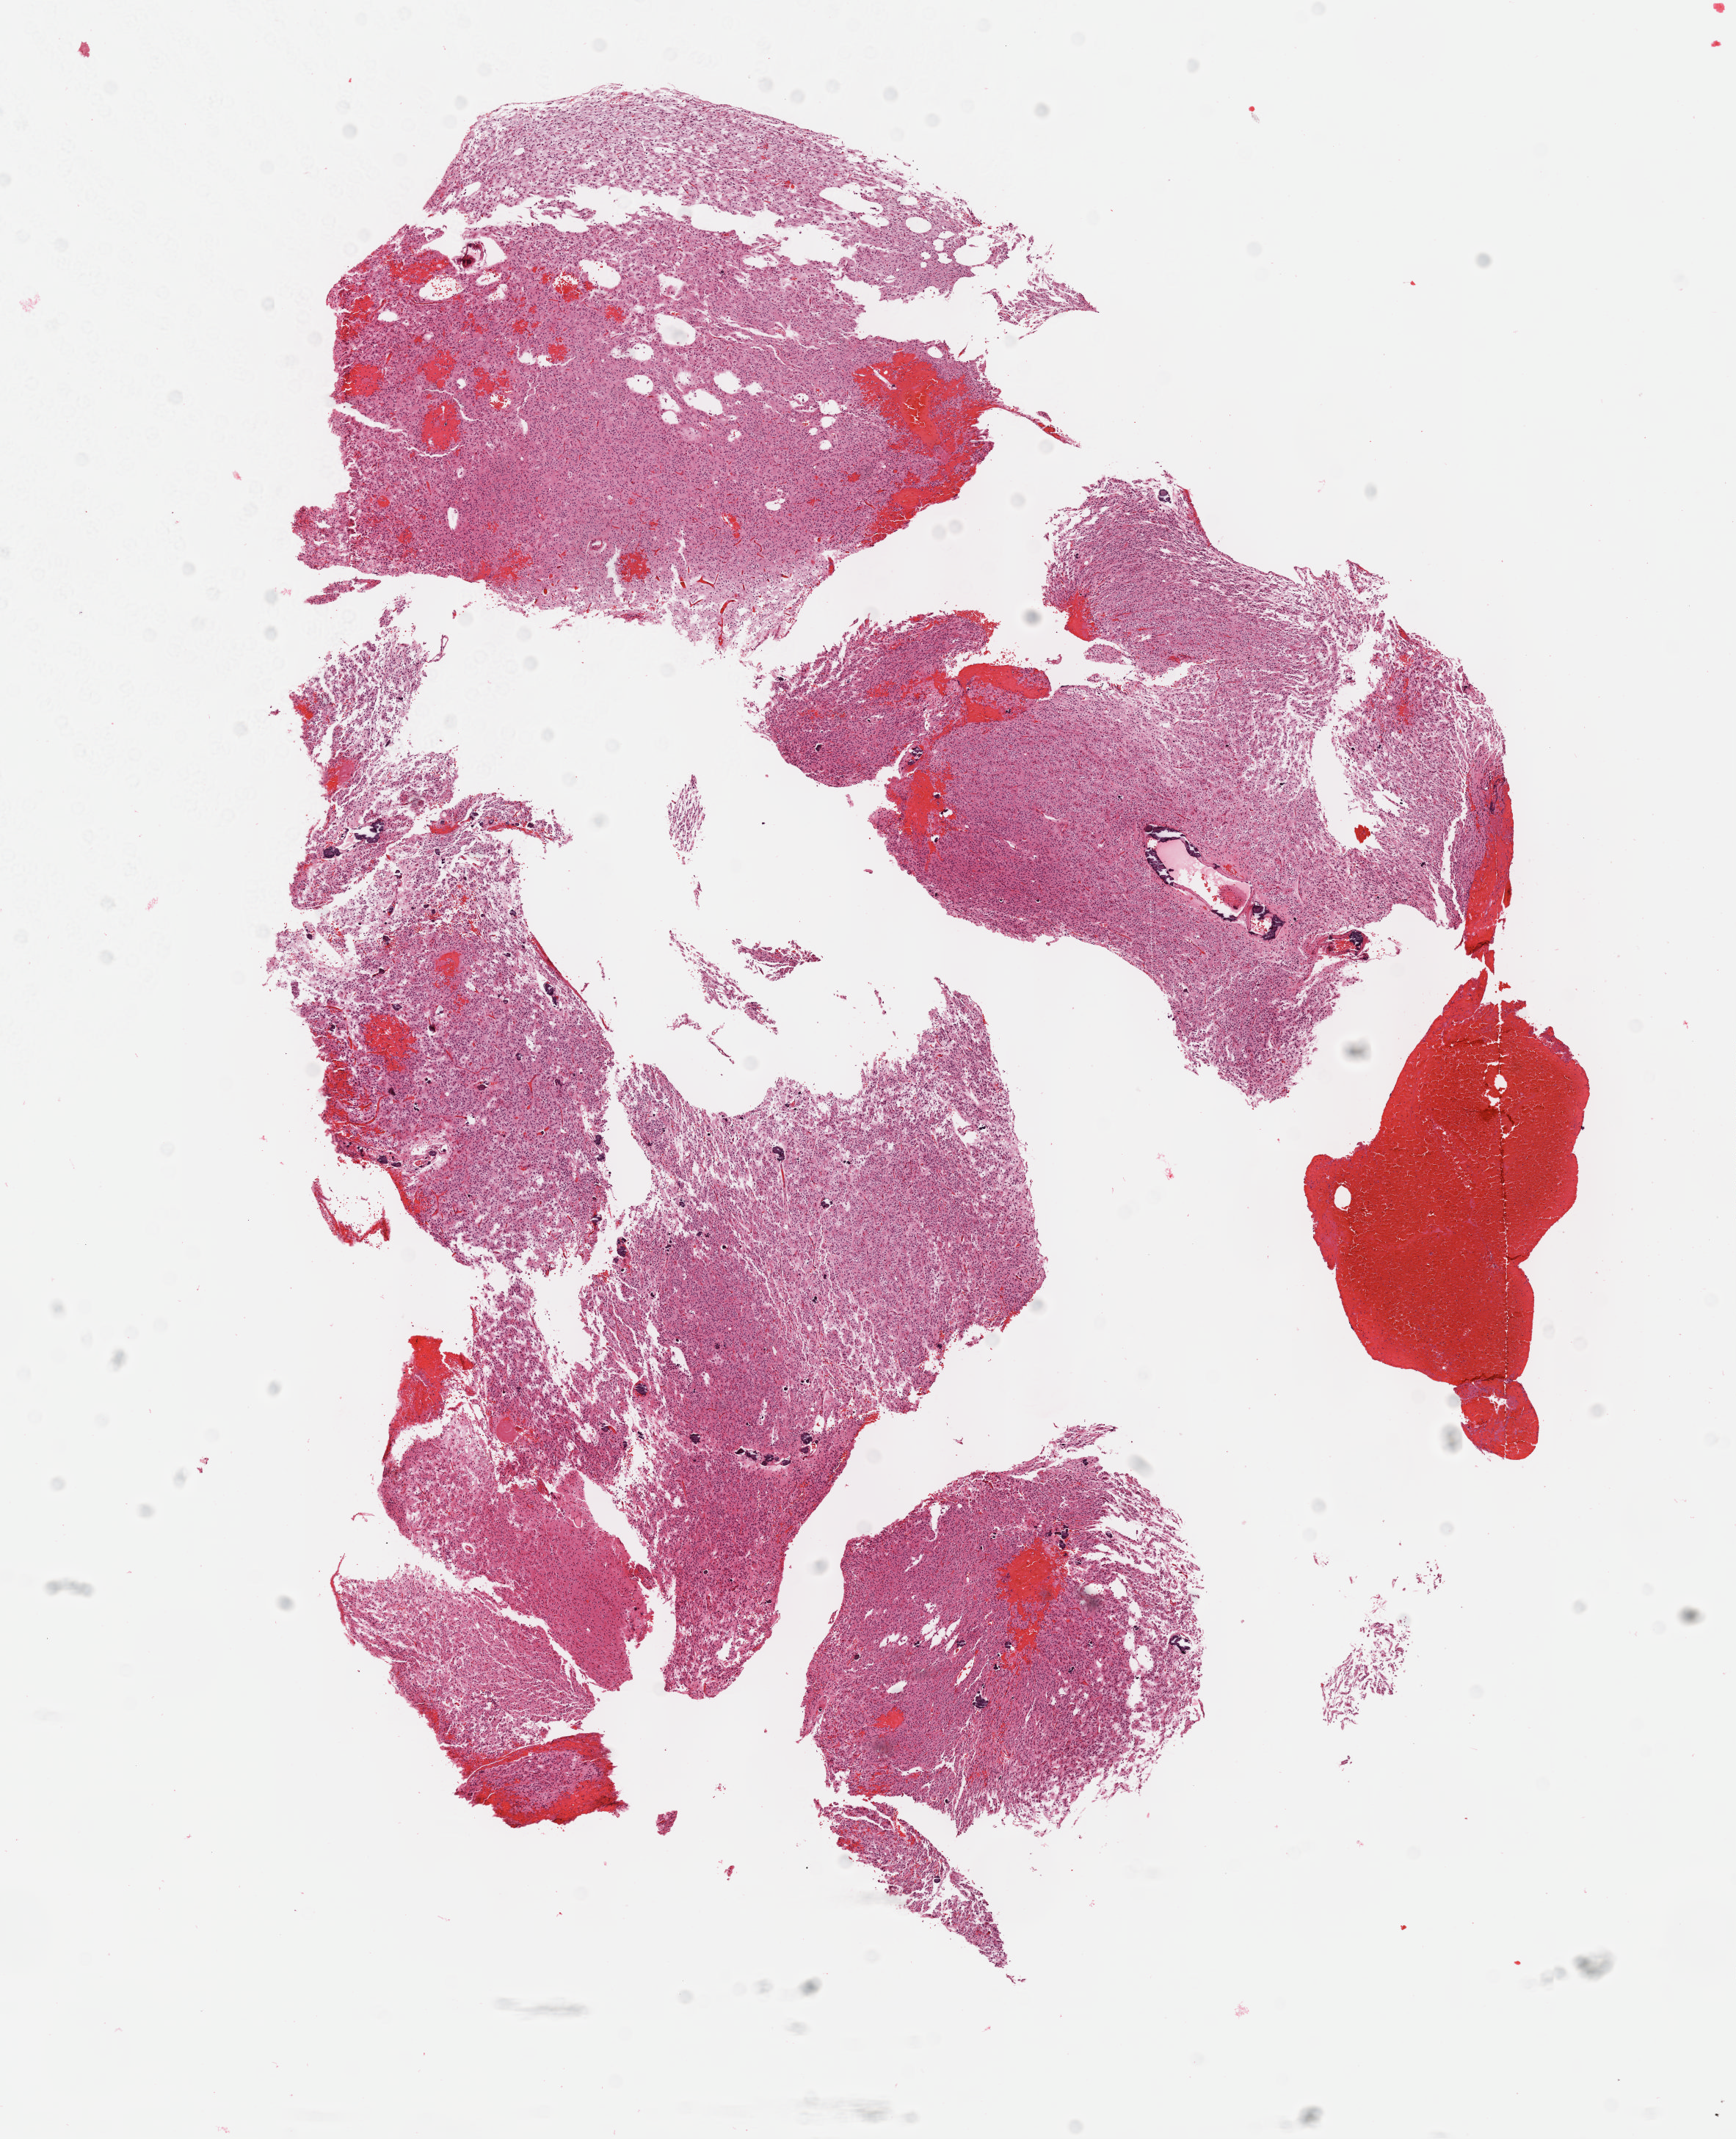
Whole-slide histology image, H&E-stained — a low-resolution overview of the entire scanned area, about 9.6 x 11.8 mm. FFPE section. Sample: primary tumour, brain. Patient: male, age at initial diagnosis 45 years. Histologic grade: G2 (moderately differentiated).
- diagnosis: Oligodendroglioma, NOS